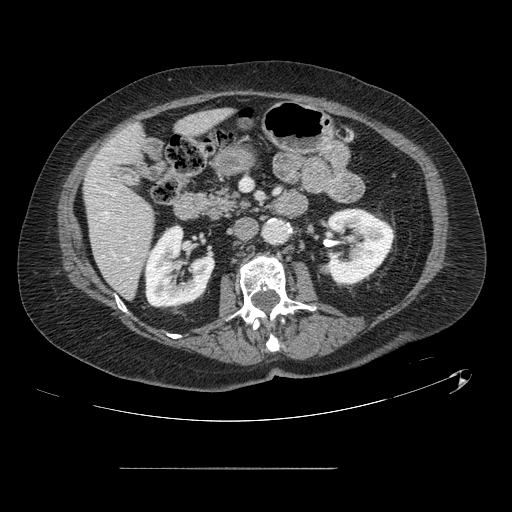
Contrast-enhanced abdominal CT, one axial slice. Position 43 of 148 along the scan axis. Intravenous contrast given. Soft-tissue window (W 400 / L 40 HU). 512 × 512 image matrix. Female patient, age 75 years. From the clinical record (not read from this slice): diagnosis: colorectal cancer liver metastases, imaged before liver resection; multiple liver metastases: no.
Outlined on this slice (manually delineated by an expert):
- hepatic veins: bounding box <105,212,129,260> (left, top, right, bottom; pixels)
- liver: <84,111,227,297>
- planned liver remnant (the part of the liver to remain after resection): <84,111,228,297>